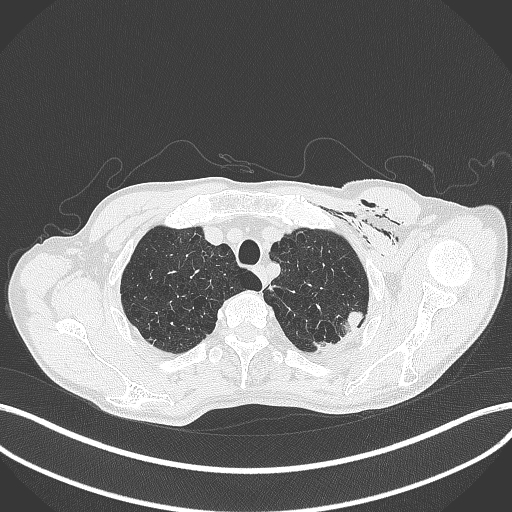
Chest CT, one axial slice; position 357 of 457 along the scan axis; 120 kVp; lung window (W 1500 / L -600 HU); 1 mm slice thickness; 512 × 512 image matrix, field of view 400 × 400 mm. Male patient, age 58 years. Case-level facts recorded for this patient, not image findings: clinical TNM (as recorded): T3 N0 M0.
Annotated regions visible in this slice (rectangle marked by the reading radiologist):
- lung tumour (recorded histology: adenocarcinoma): bounding box <344,309,368,335> (left, top, right, bottom; pixels)